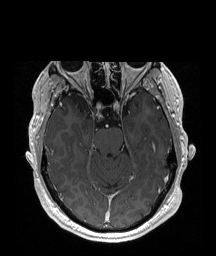
Brain MRI from a brain-tumour surgery series, one axial slice; T1-weighted post-contrast; 1 mm slice thickness; 216 × 256 image matrix, field of view 219 × 260 mm. From the clinical record (not read from this slice): histopathology: Astrocytoma; WHO grade: 2; IDH mutation: yes.
Annotated regions visible in this slice (expert manual segmentation):
- tumour: box from (x=68, y=93) to (x=91, y=113) px